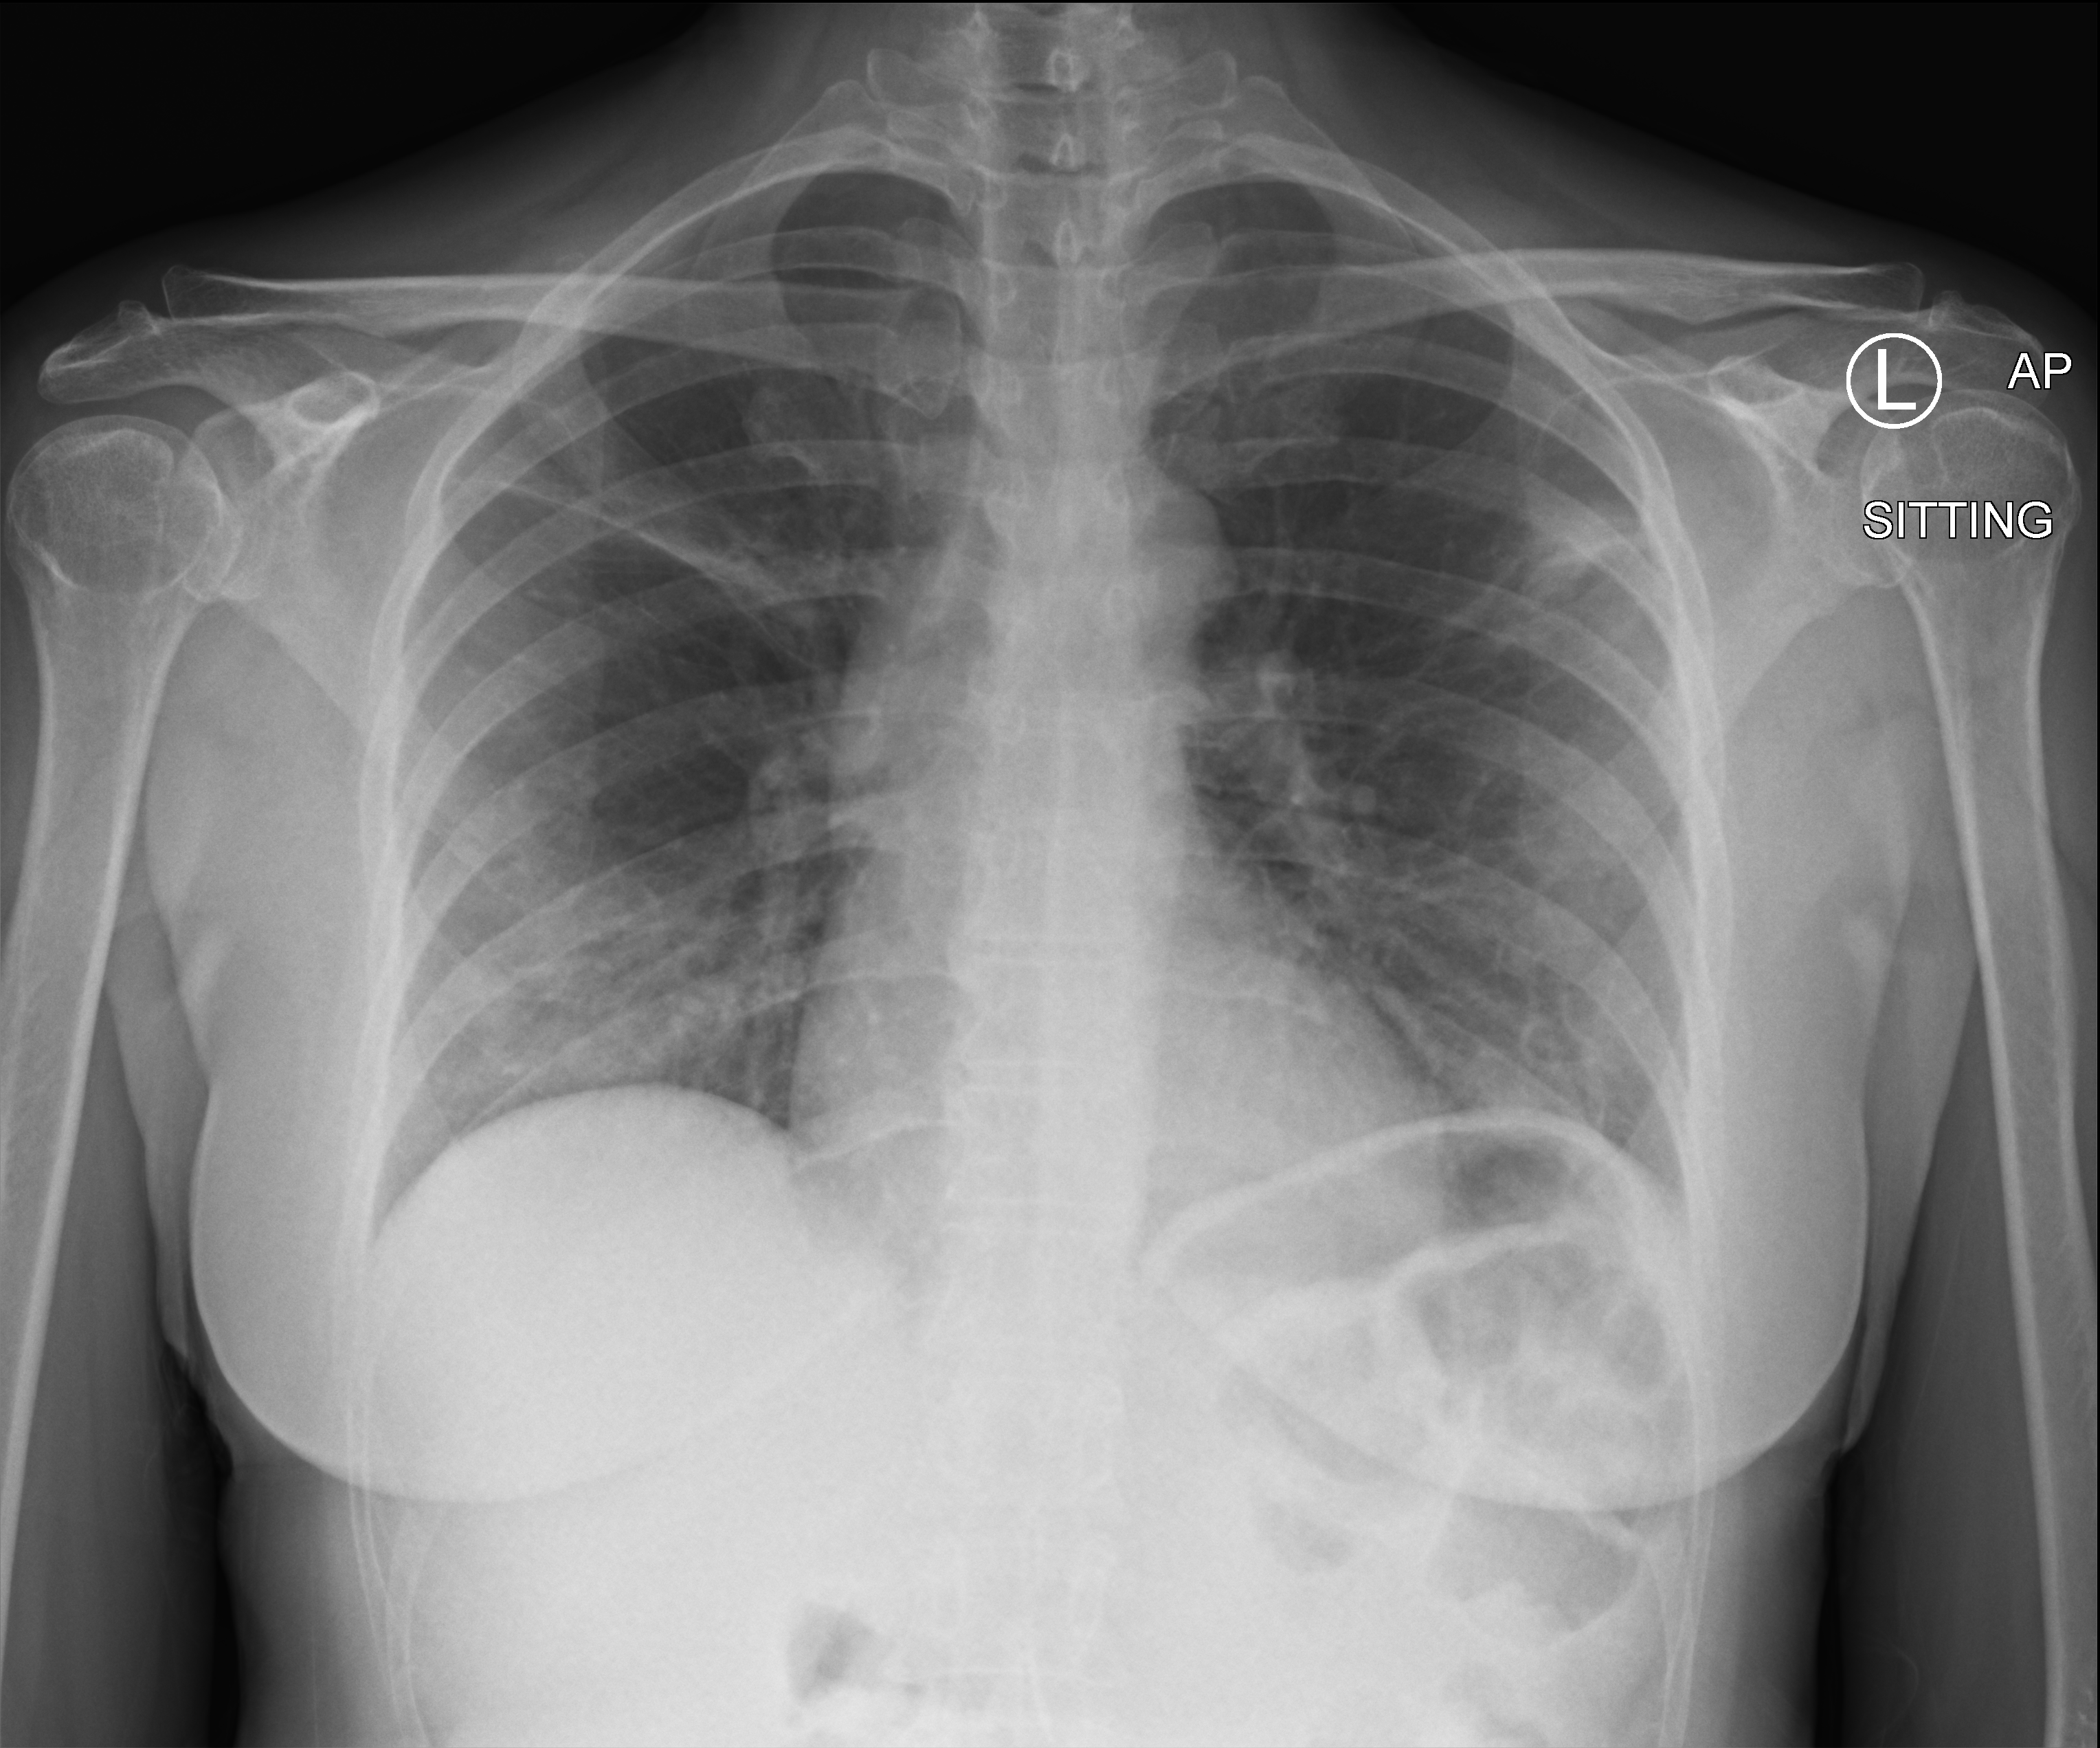
Portable chest radiograph, anteroposterior (AP) projection. Female patient hospitalised with COVID-19, age 18–59 years.
From the hospital-stay record, not from the radiograph (when in the stay this image was taken is not recorded): hypertension (admission record): no.